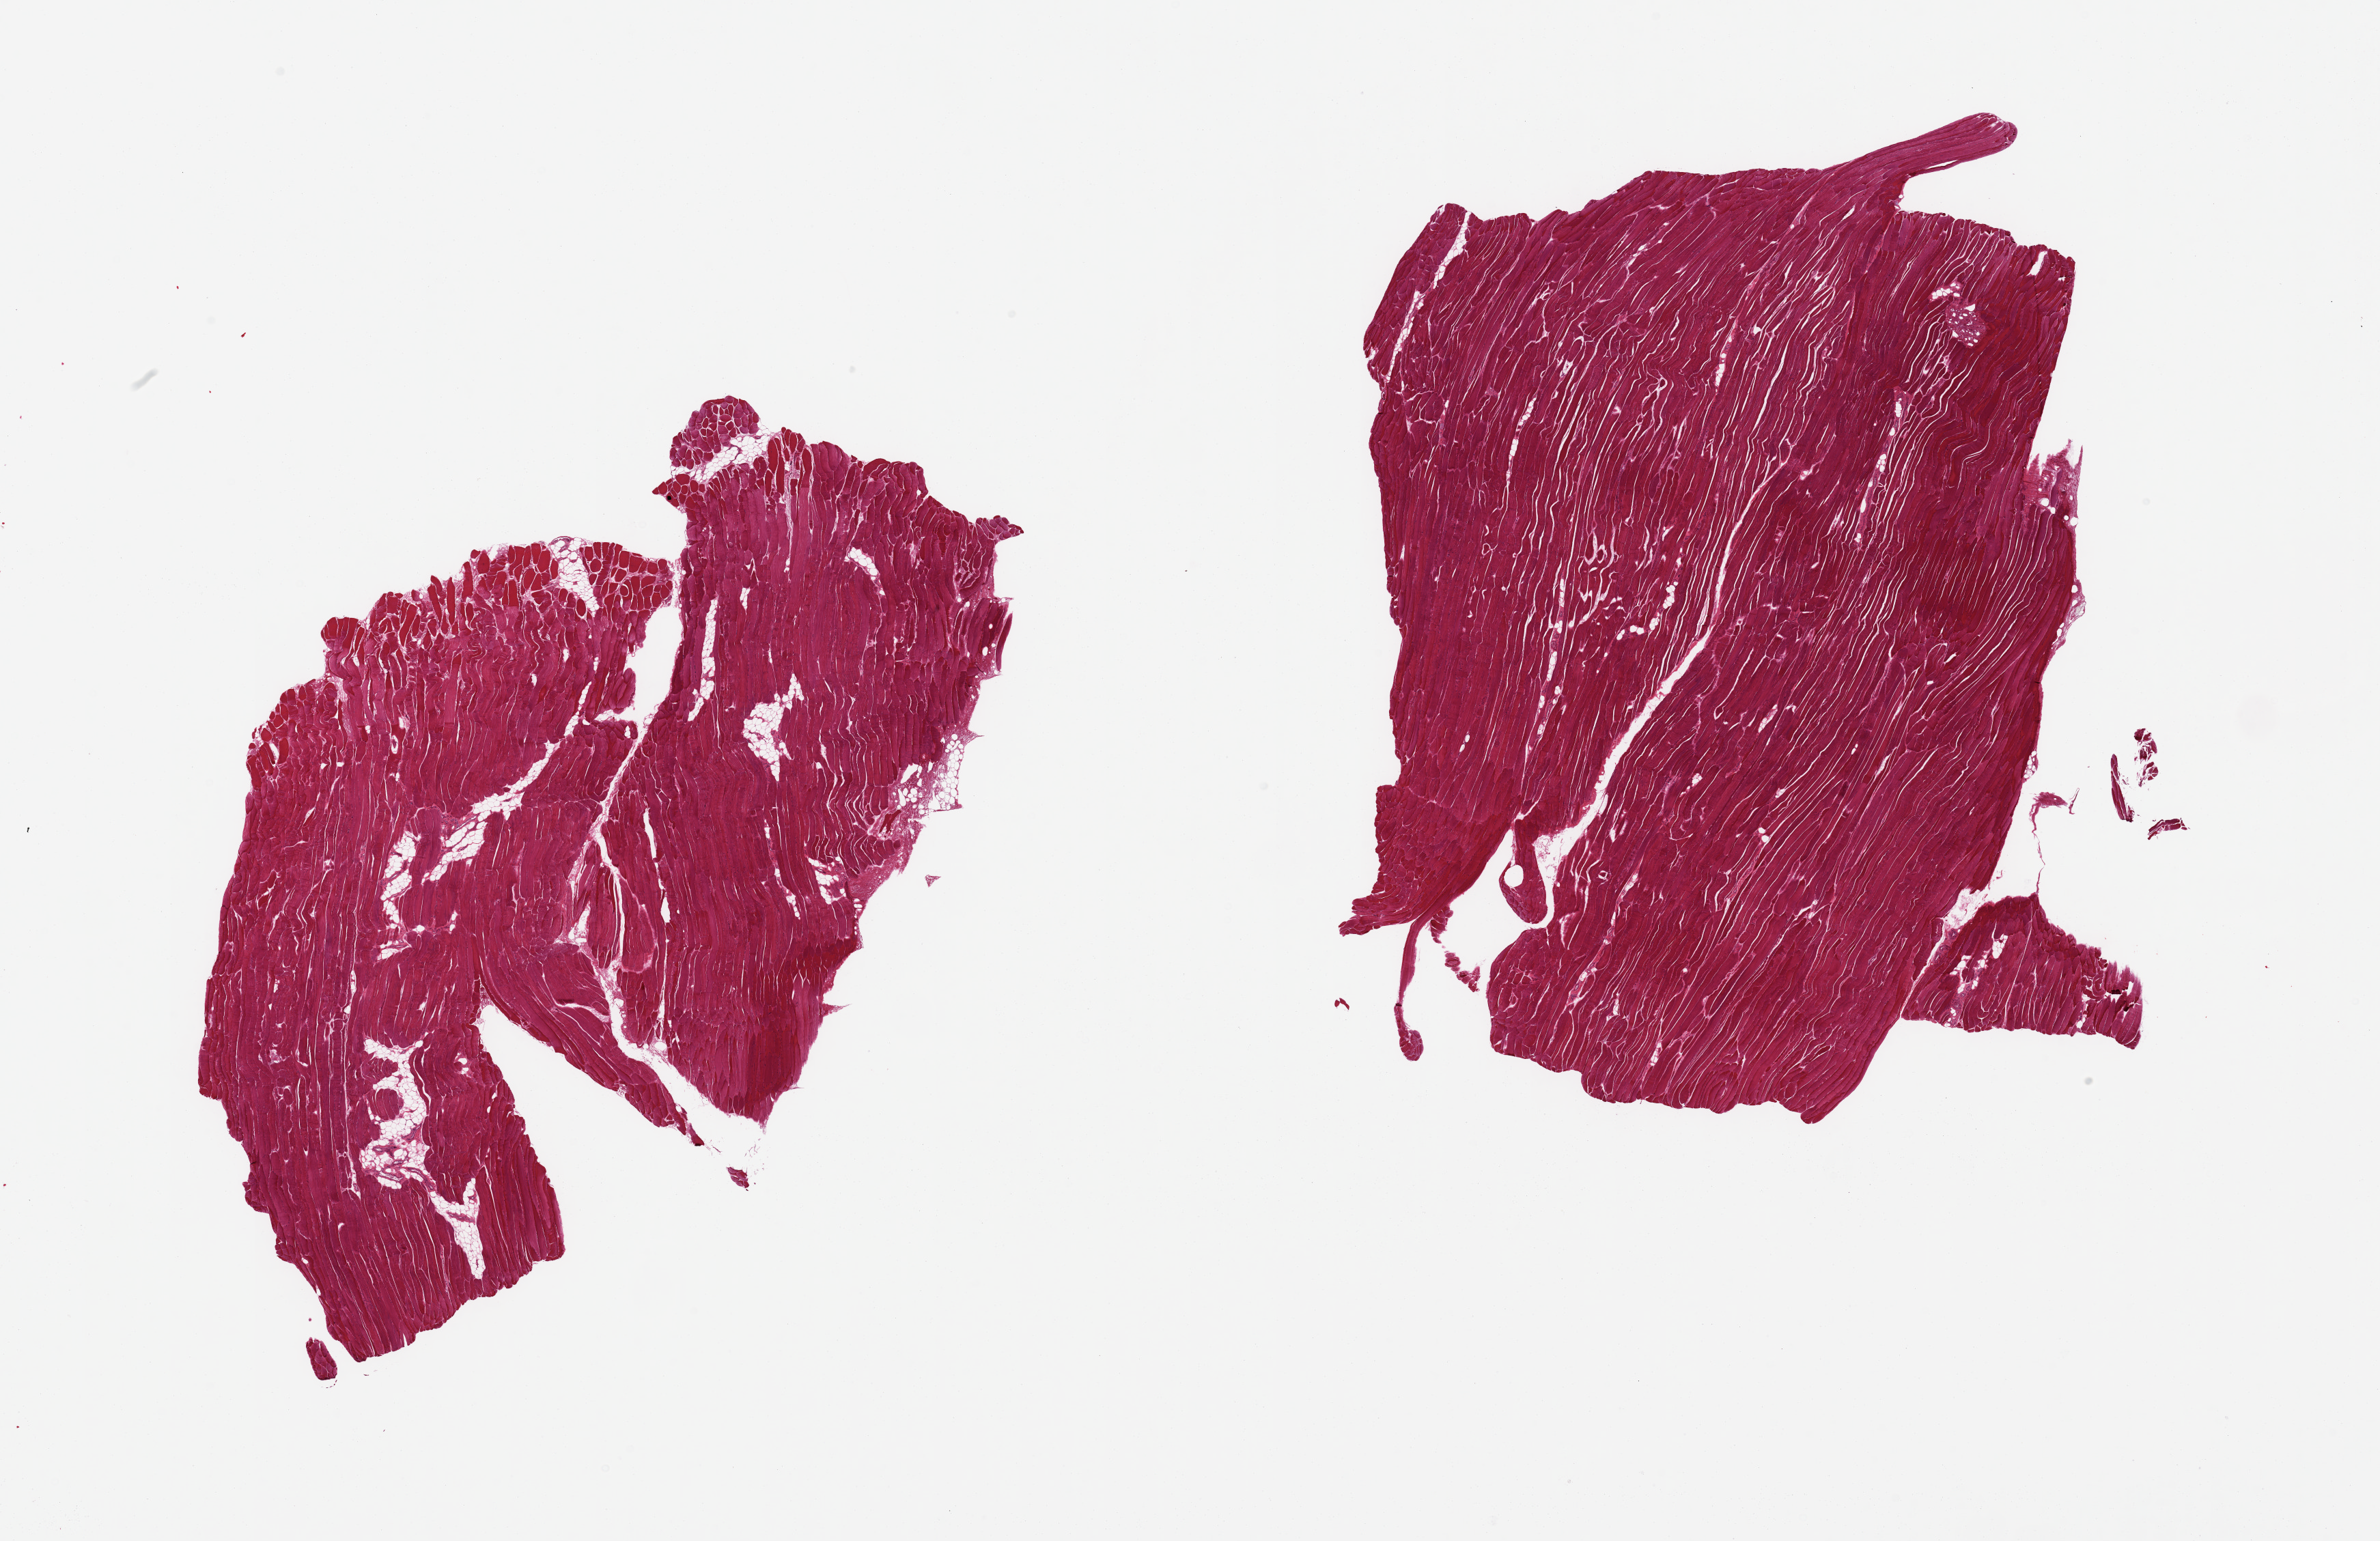
Digitized hematoxylin and eosin (H&E)-stained section, whole scanned area (about 27.6 x 17.9 mm, acquisition: 20x scan) shown as a low-resolution overview, PAXgene-fixed, paraffin-embedded tissue, target tissue: skeletal muscle, donor tissue sample. Donor: male.
* review note (as recorded): 2 pieces; ~10% and 5% internal fat